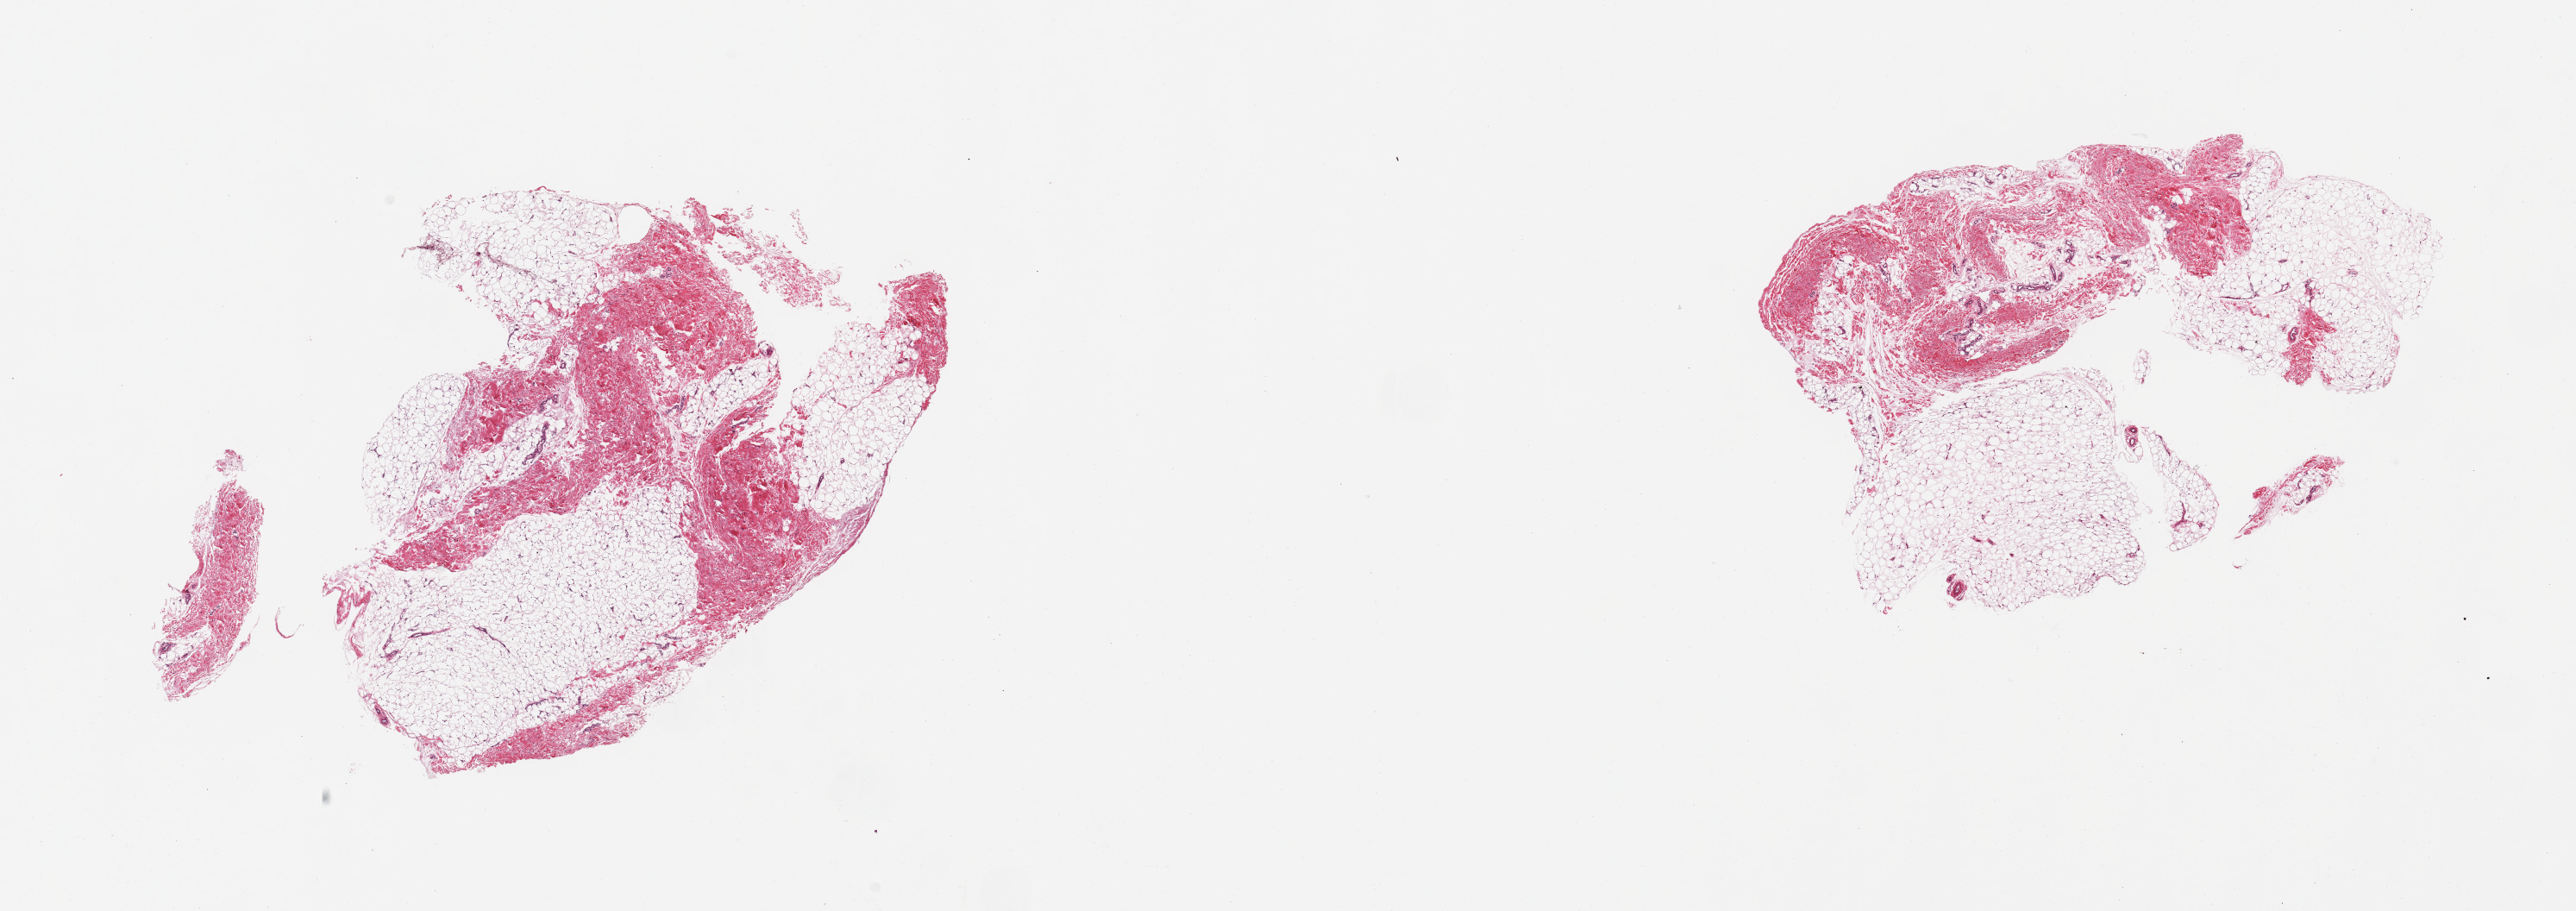
Whole-slide image, haematoxylin and eosin stain — whole scanned area (about 23.6 x 8.4 mm) shown as a low-resolution overview. PAXgene-fixed paraffin-embedded (PFPE) section. Section of breast (target tissue). Donor tissue sample. Donor: male.
* review note (as recorded): 2 pieces, fibroadipose elements